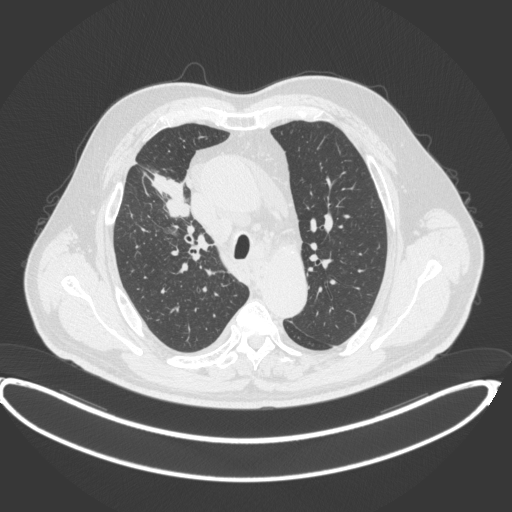
Chest CT, one axial slice. Position 289 of 395 along the scan axis. Reconstruction kernel B31f. Lung window (W 1500 / L -600 HU). 1 mm slice thickness. 512 × 512 image matrix, field of view 448 × 448 mm. Male patient, age 62 years. Case-level facts recorded for this patient, not image findings: clinical TNM (as recorded): T1c N3 M1c.
Structures marked on this image (rectangle marked by the reading radiologist):
- lung tumour (recorded histology: adenocarcinoma): box from (x=151, y=167) to (x=192, y=216) px